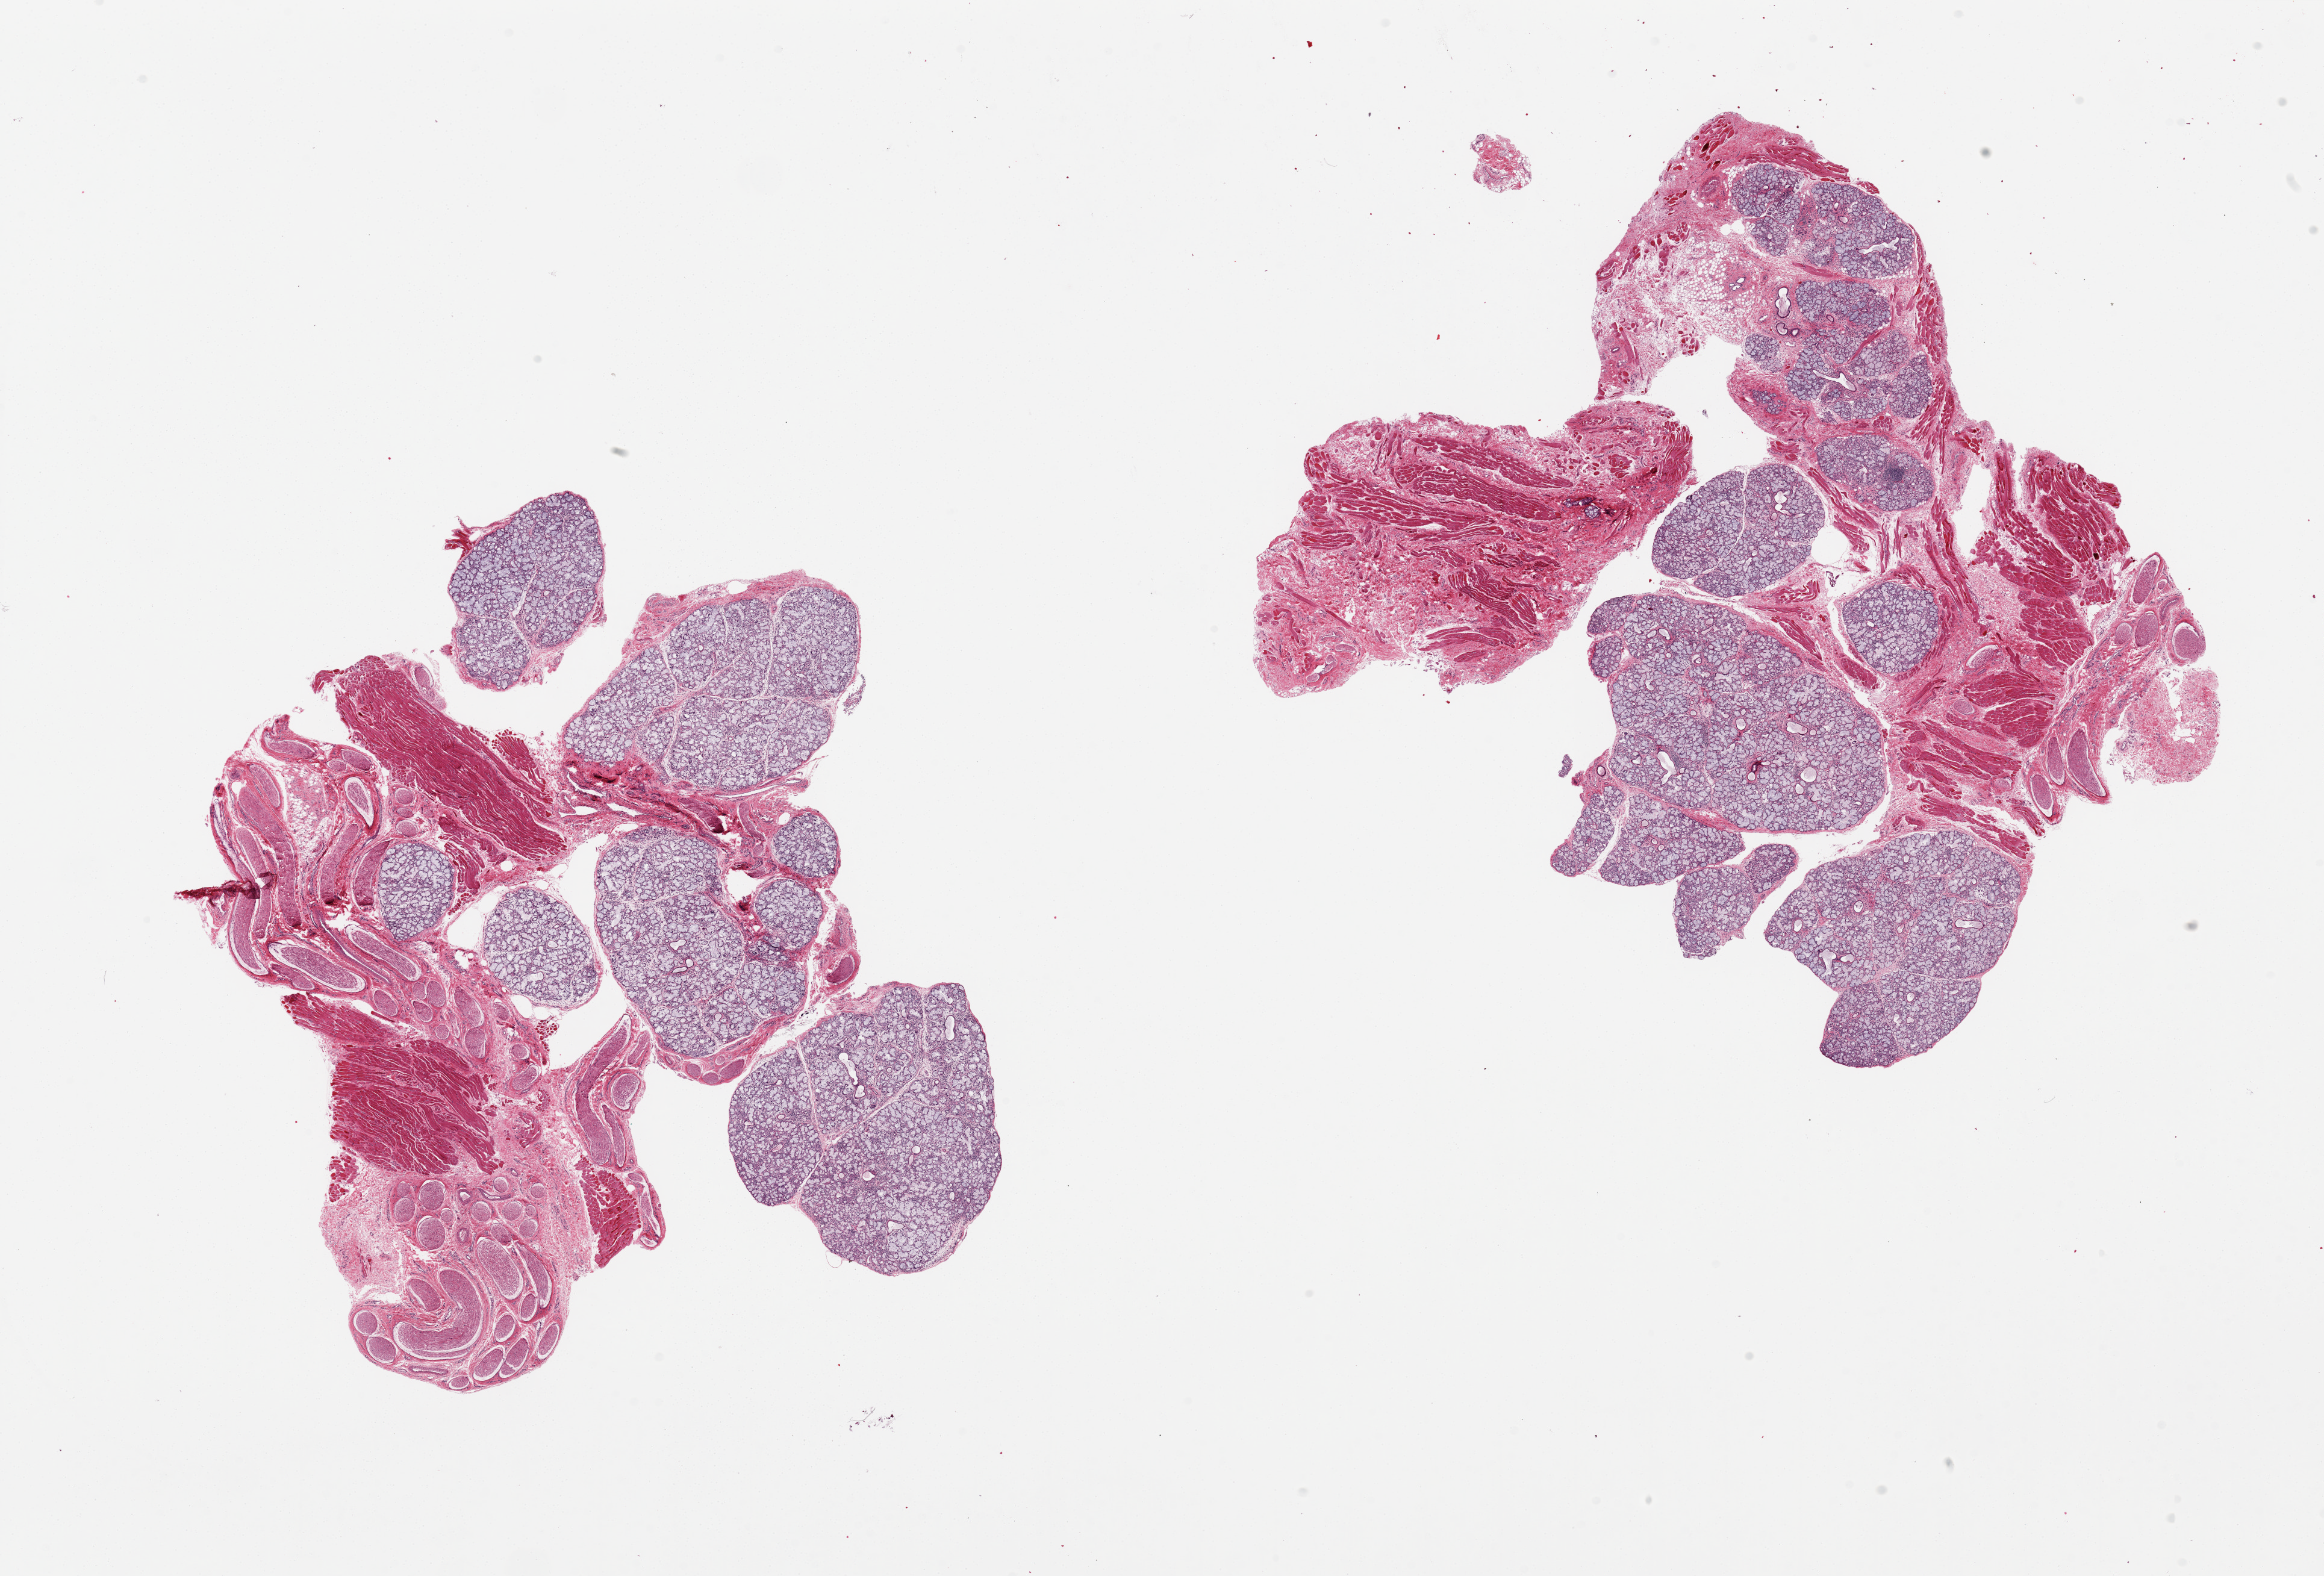
H&E whole-slide image — a low-resolution overview of the entire scanned area, about 30.5 x 20.7 mm (acquisition: 20x scan); PAXgene-fixed, paraffin-embedded tissue; target tissue: minor salivary gland; tissue donor sample. Donor sex: male.
Review note (as recorded): 2 pieces, both ~50% glandular tissue; rest is fibromuscular stroma.